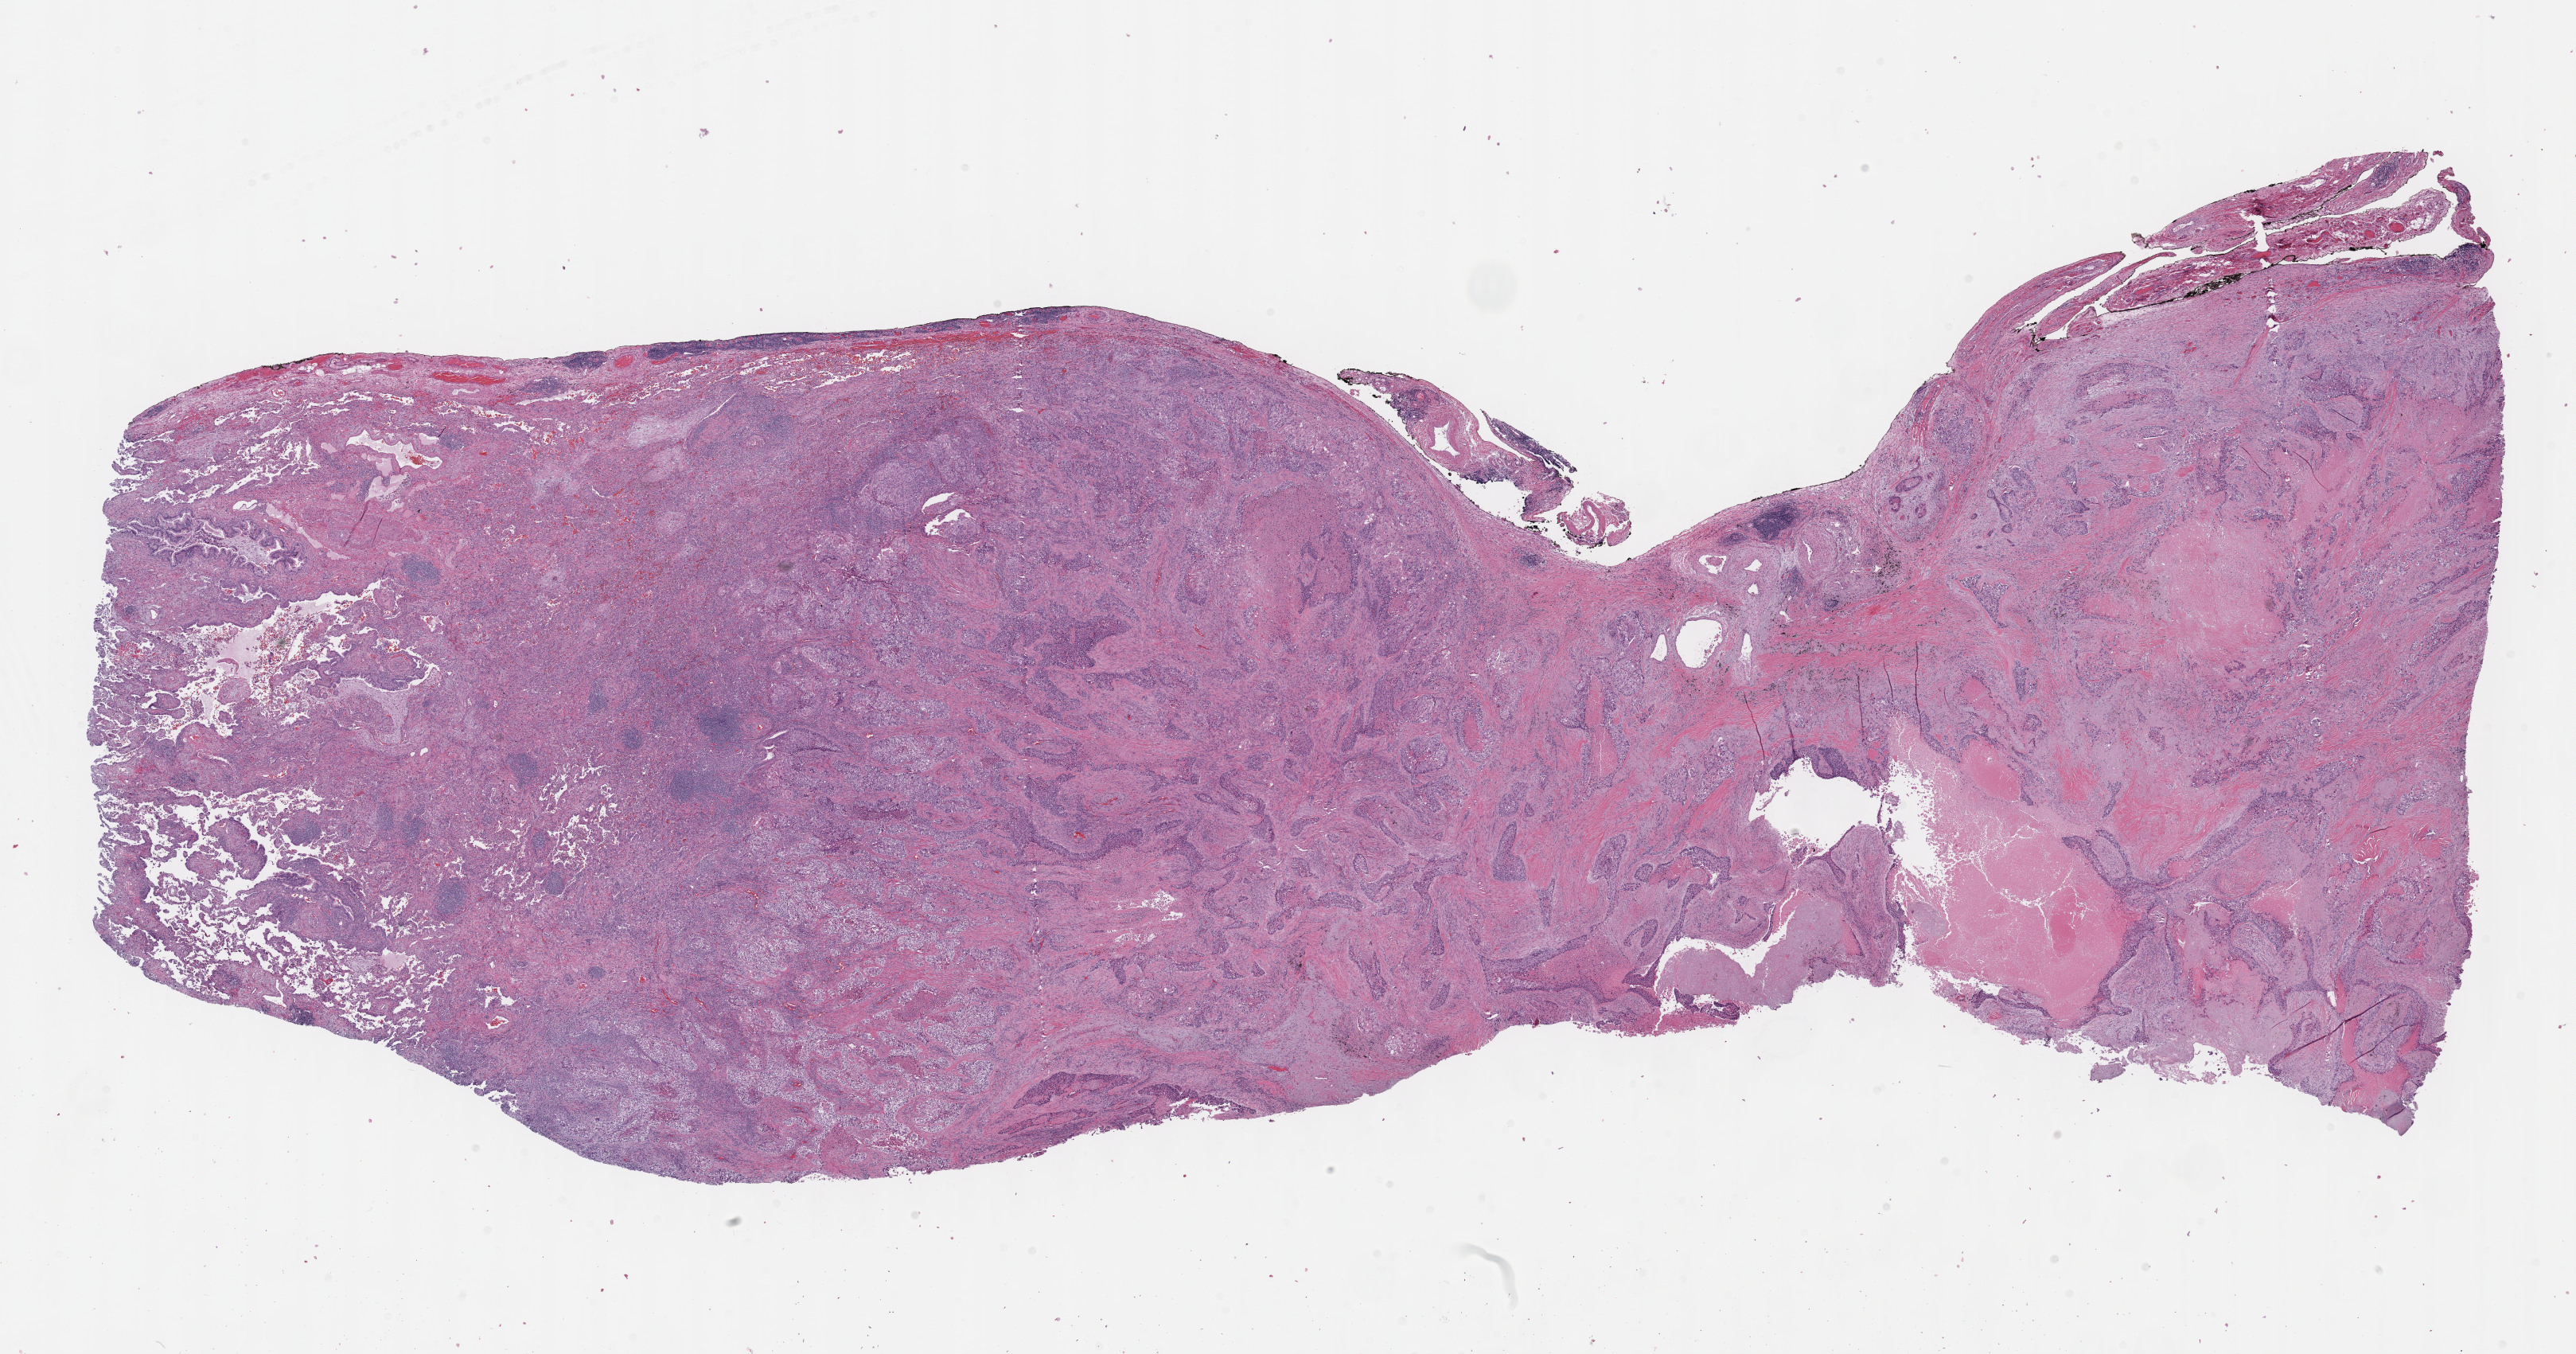
Digitized H&E-stained tissue section (whole slide), whole scanned area (about 26.2 x 13.7 mm, slide scanned at 40x) shown as a low-resolution overview, formalin-fixed paraffin-embedded (FFPE) diagnostic section, lung, primary tumour sample. Male, age 79 years at initial diagnosis.
Pathologic diagnosis: Squamous cell carcinoma, NOS (lower lobe, lung).